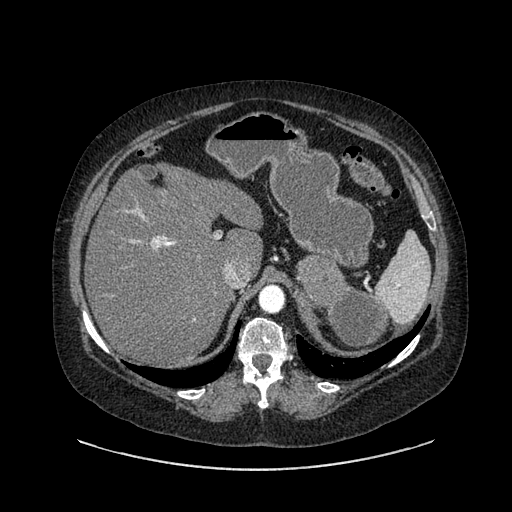
Contrast-enhanced abdominal CT, one axial slice. Slice 618 of 769 in the series (ordered by position). Reconstruction kernel SOFT. 120 kVp. Intravenous contrast given. Soft-tissue window (W 400 / L 40 HU). 0.62 mm slice thickness. 512 × 512 image matrix, field of view 460 × 460 mm. Patient: female, 61 years. From the clinical record (not read from this slice): diagnosis: adrenocortical carcinoma; tumour side: left adrenal; tumour size at pathology: 13 cm; Ki-67 index: 79 %; stage (as recorded): 2.
Outlined on this slice (semi-automatic segmentation, software-assisted and operator-edited):
- mass: bounding box (x1, y1, x2, y2) in pixels: (298, 257, 389, 349)